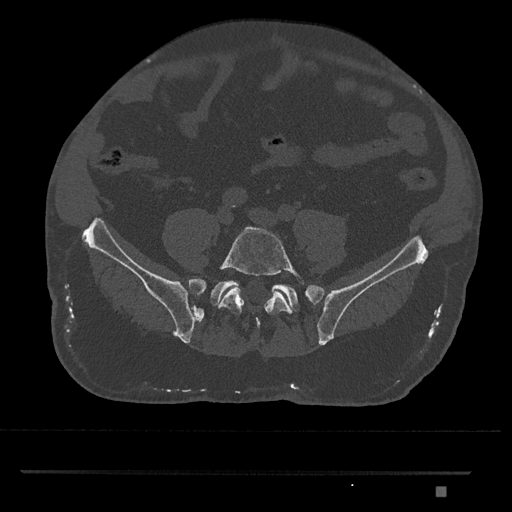
CT including the spine, one axial slice. Position 543 of 1134 along the scan axis. Bone window (W 1800 / L 400 HU). 0.5 mm slice thickness. 512 × 512 image matrix, field of view 429 × 429 mm. Male patient, age 65 years. From the clinical record (not read from this slice): primary cancer: prostate.
Outlined on this slice (semi-automatically segmented with operator editing):
- L5 vertebra: bounding box [x1, y1, x2, y2] px = [218, 226, 306, 329]